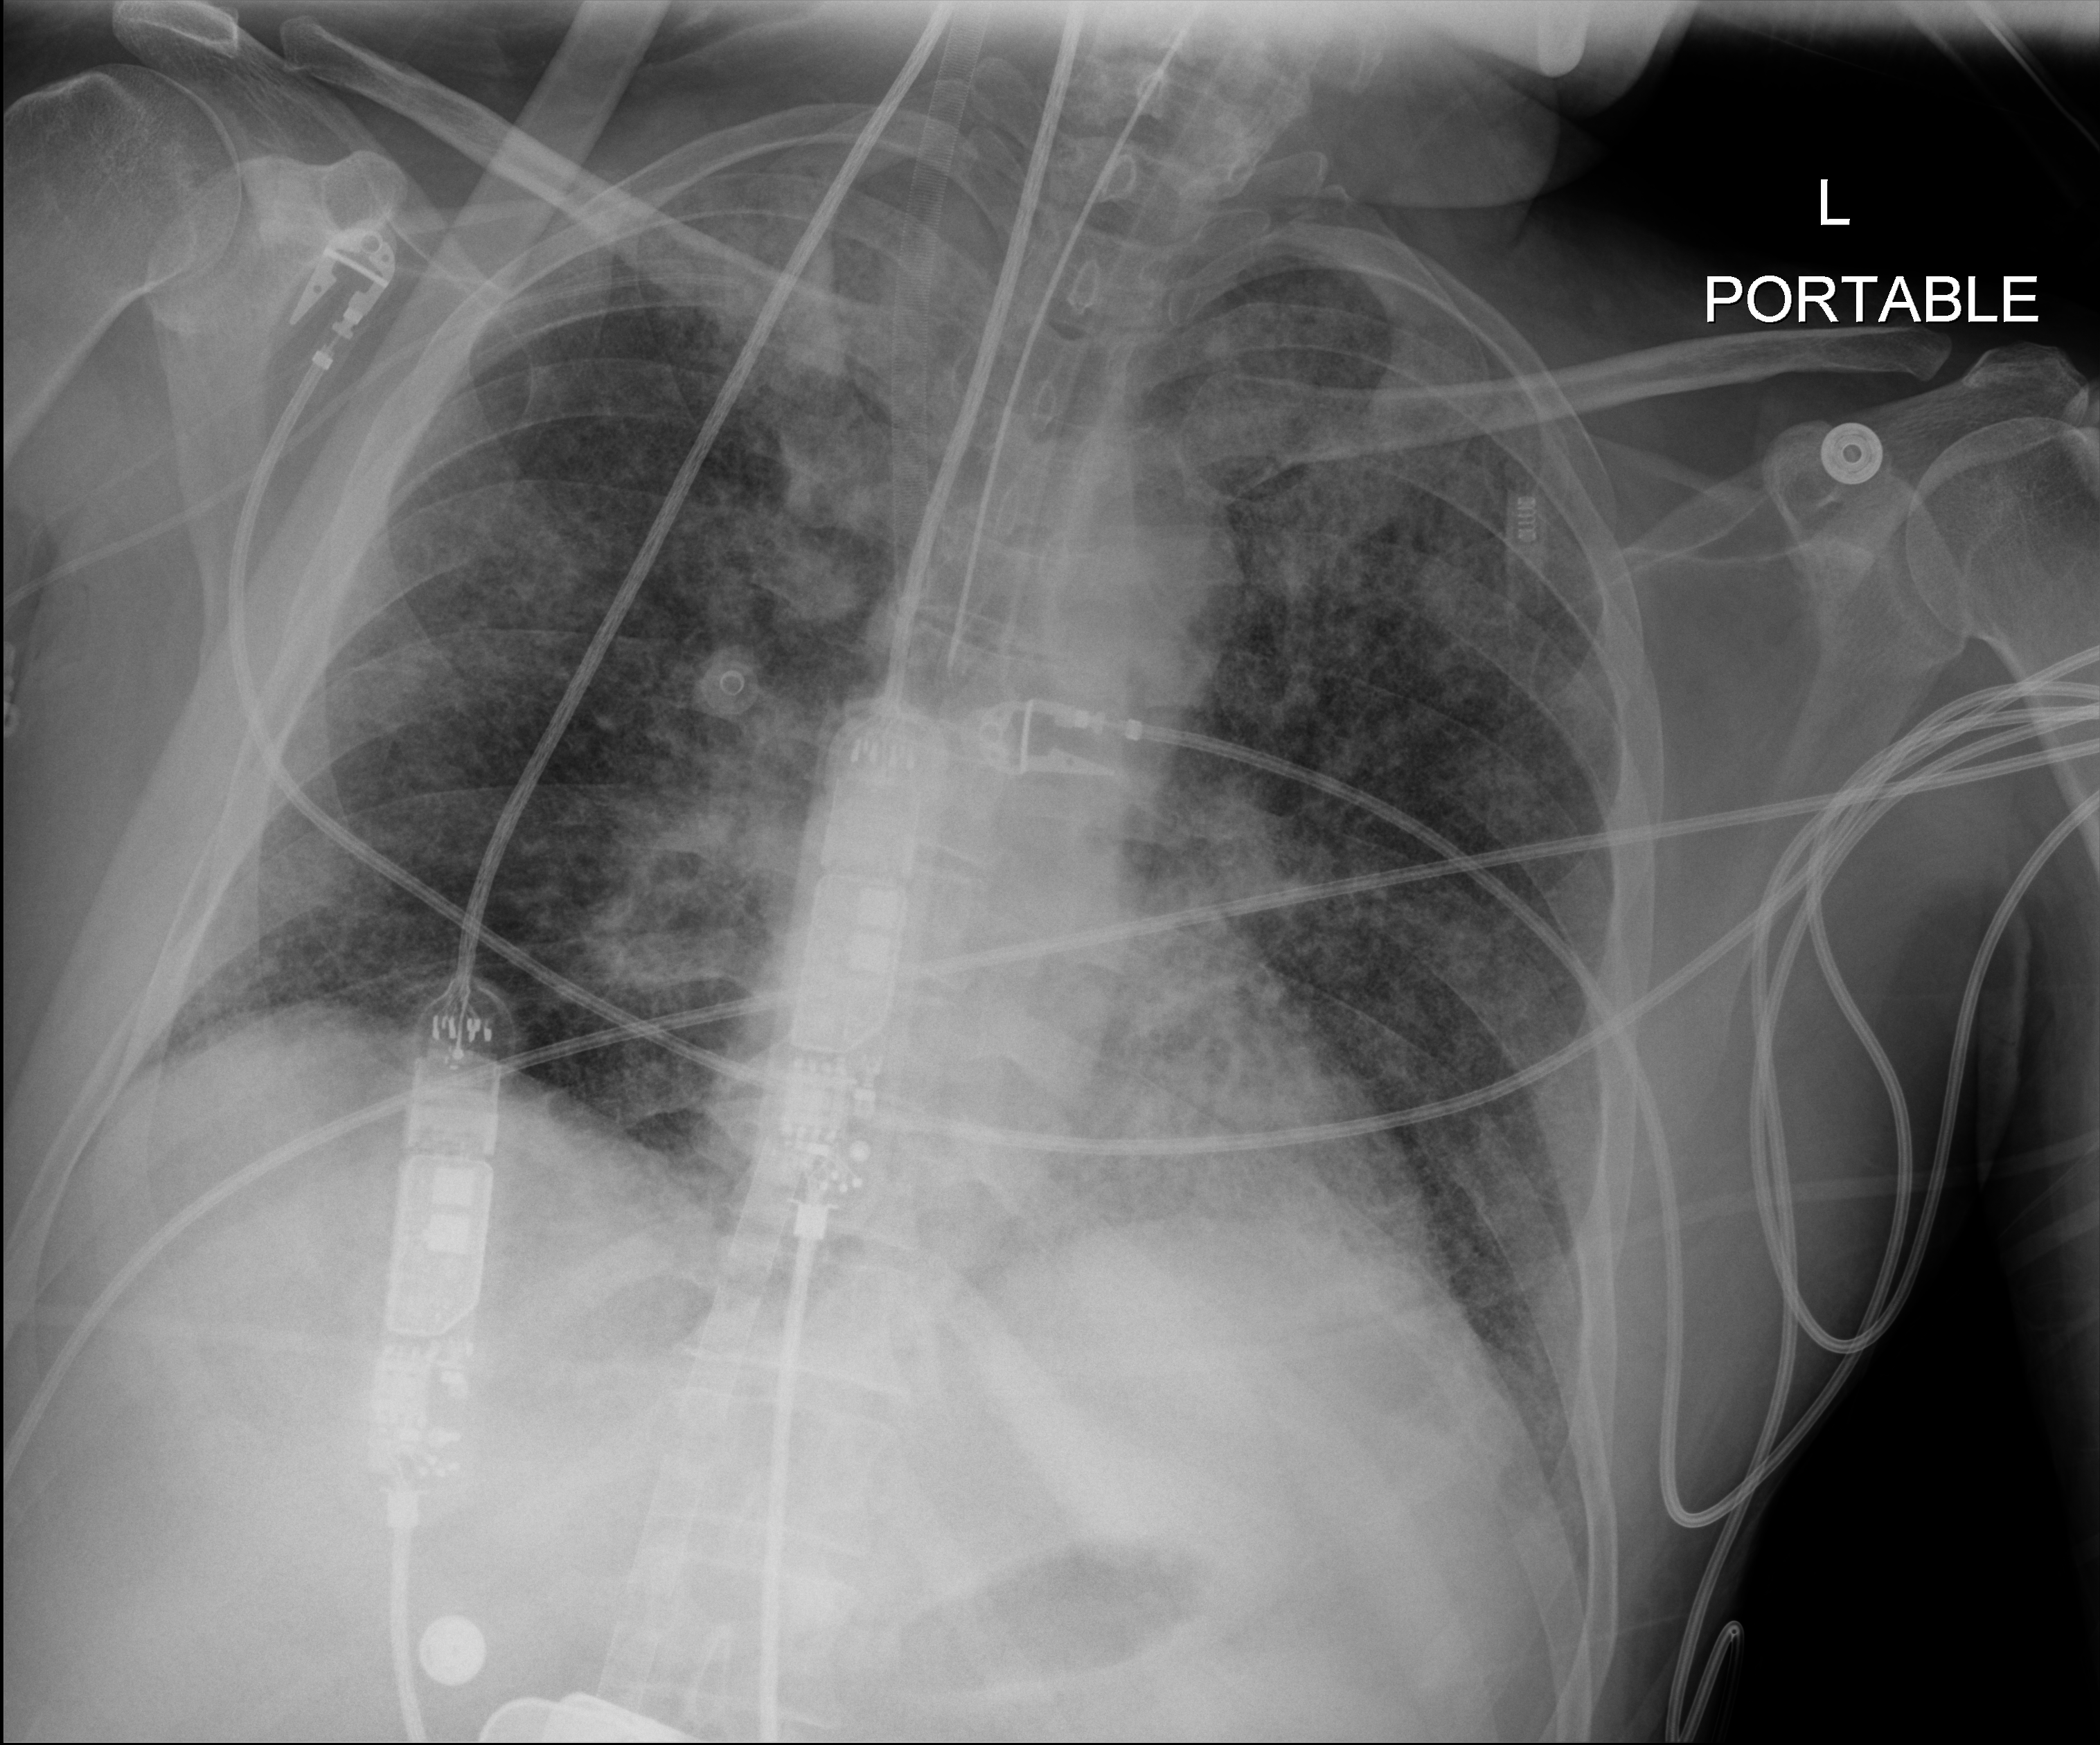
Bedside chest radiograph (digital radiography), anteroposterior (AP) projection. Patient hospitalised with COVID-19; male, aged 18–59 years.
Admission-level facts for this patient (not findings on this image; timing relative to this image not recorded): hypertension (admission record): no; smoking status (admission record): never.